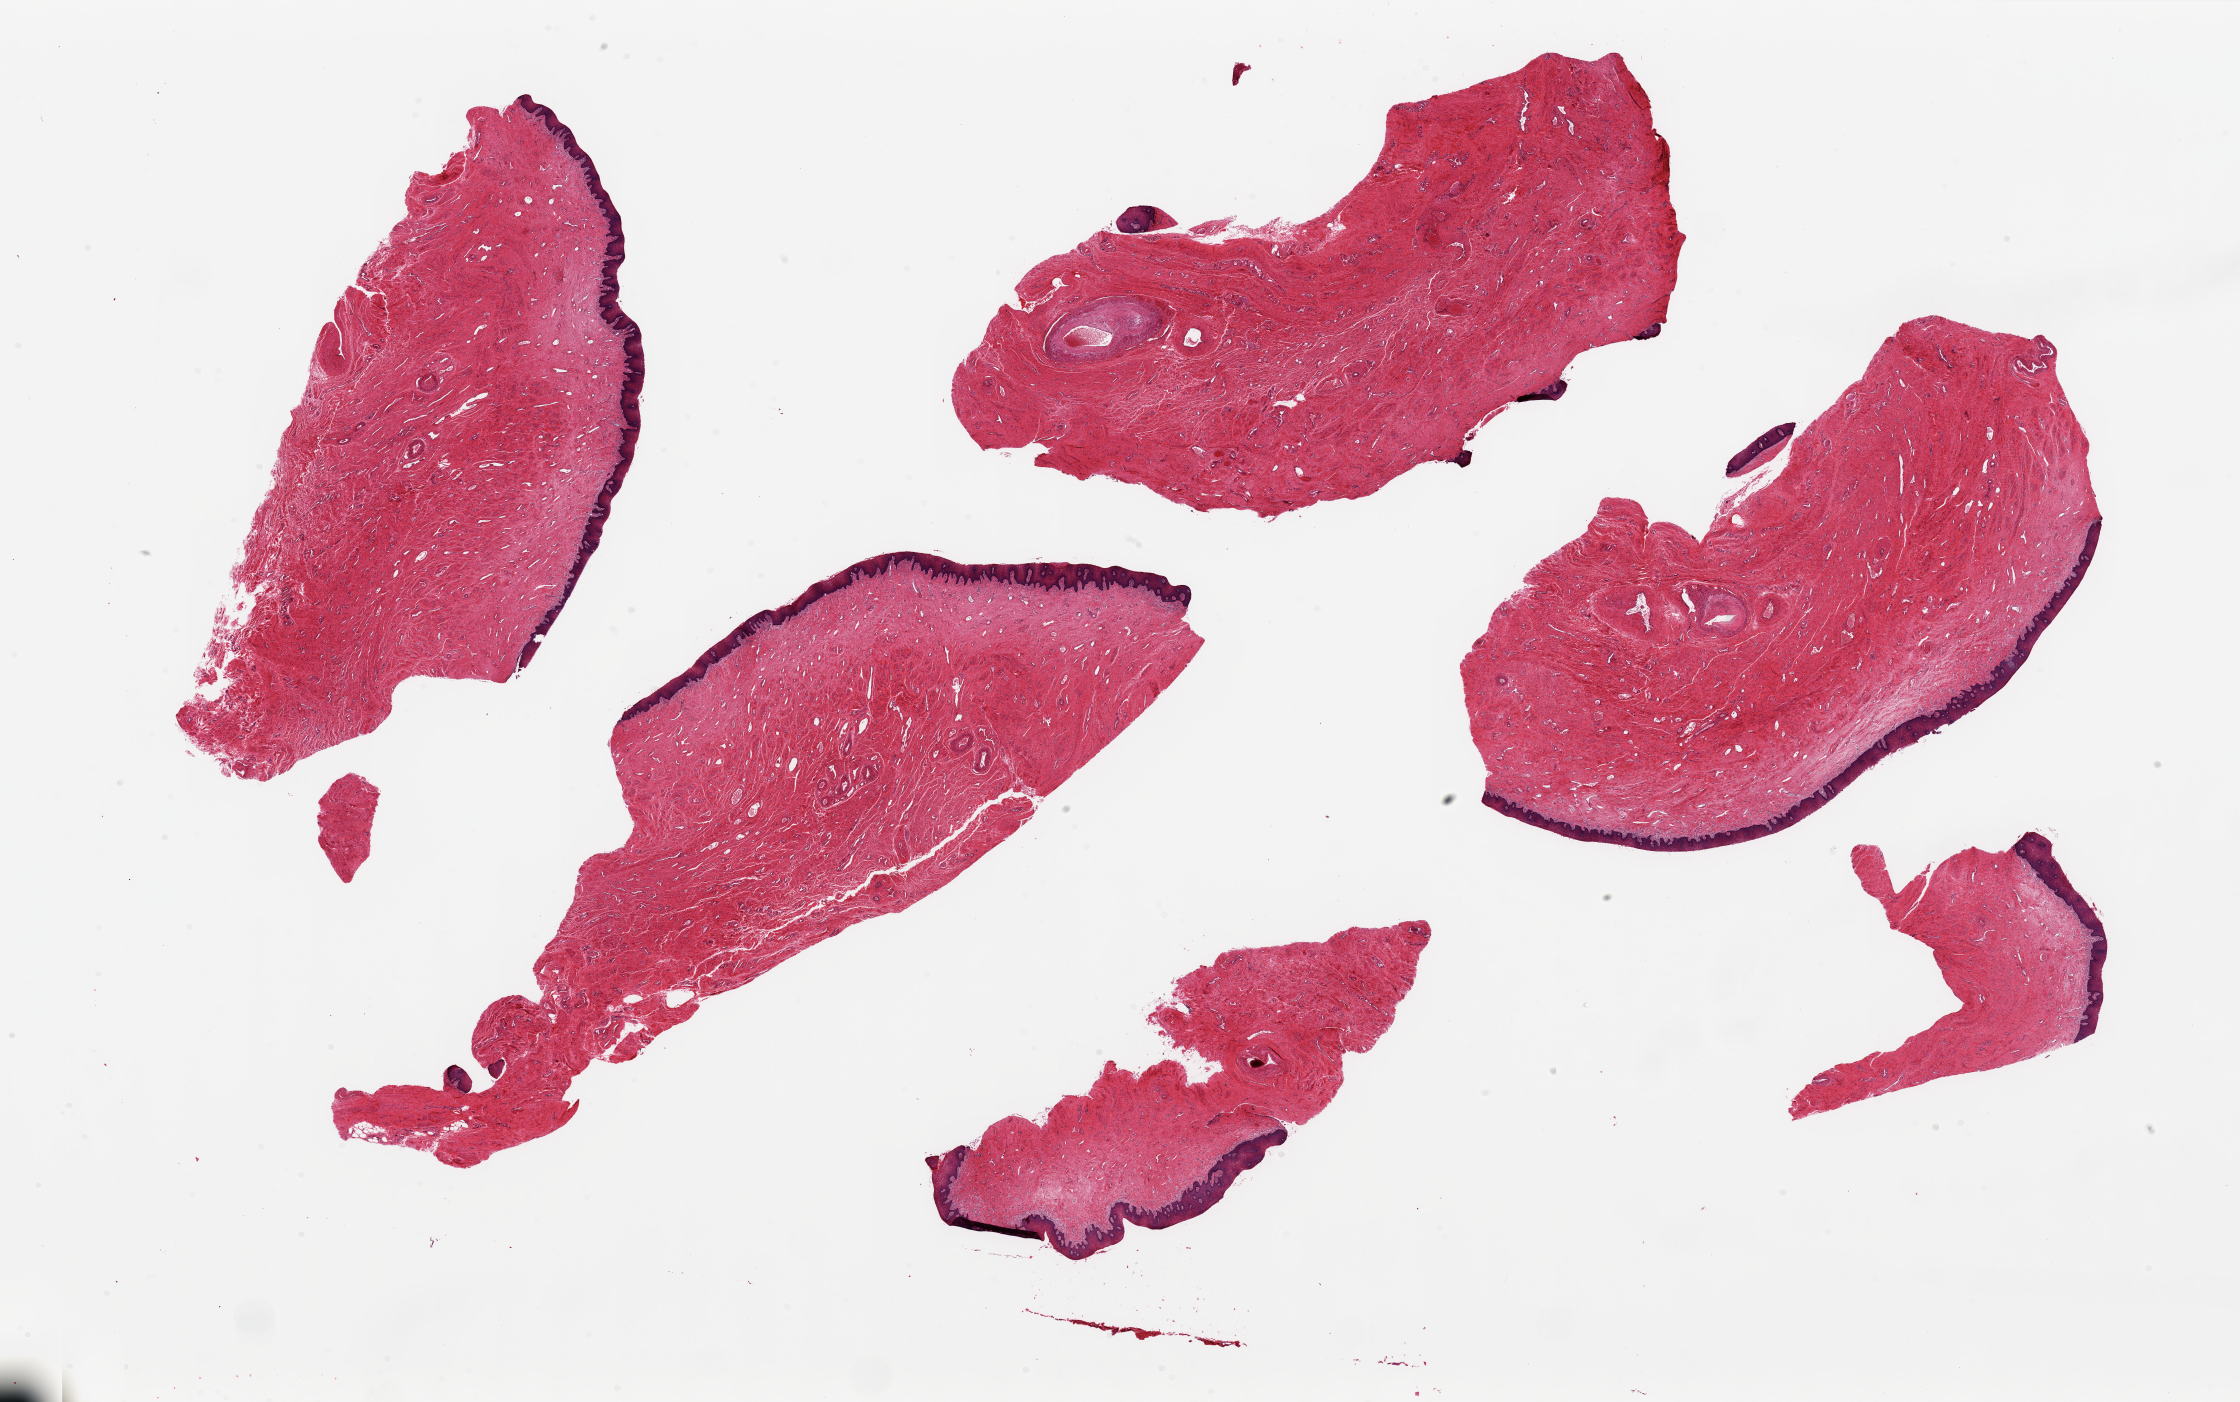
Hematoxylin and eosin (H&E) whole-slide image — a low-resolution overview of the entire scanned area, about 35.4 x 22.2 mm. PAXgene-fixed, paraffin-embedded tissue. Sampled site (target tissue): vagina. Tissue donor sample. Donor: female.
Review note (as recorded): 4~ 10x4mm pieces + fragments. Squamous epithelium is 3-5% of specimen thickness.